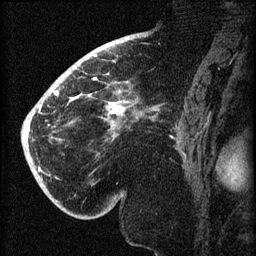
Breast MRI (dynamic contrast-enhanced), one sagittal slice. Position 43 of 60 along the scan axis. Dynamic contrast-enhanced series, image 2 of 3 at this slice position (ordered by acquisition). 1.5 T. TE 4.2 ms, TR 8.2 ms. 256 × 256 image matrix, field of view 180 × 180 mm. Patient: female, 71 years.
Structures marked on this image (semi-automatic segmentation, software-assisted and operator-edited):
- analysis volume of interest (the breast-tissue region the enhancement analysis was run in; not a lesion): box from (x=40, y=72) to (x=147, y=196) px
- tumour enhancement mask (voxels above the 70 % enhancement threshold inside the analysis volume of interest): (x=40, y=78)–(x=127, y=115)